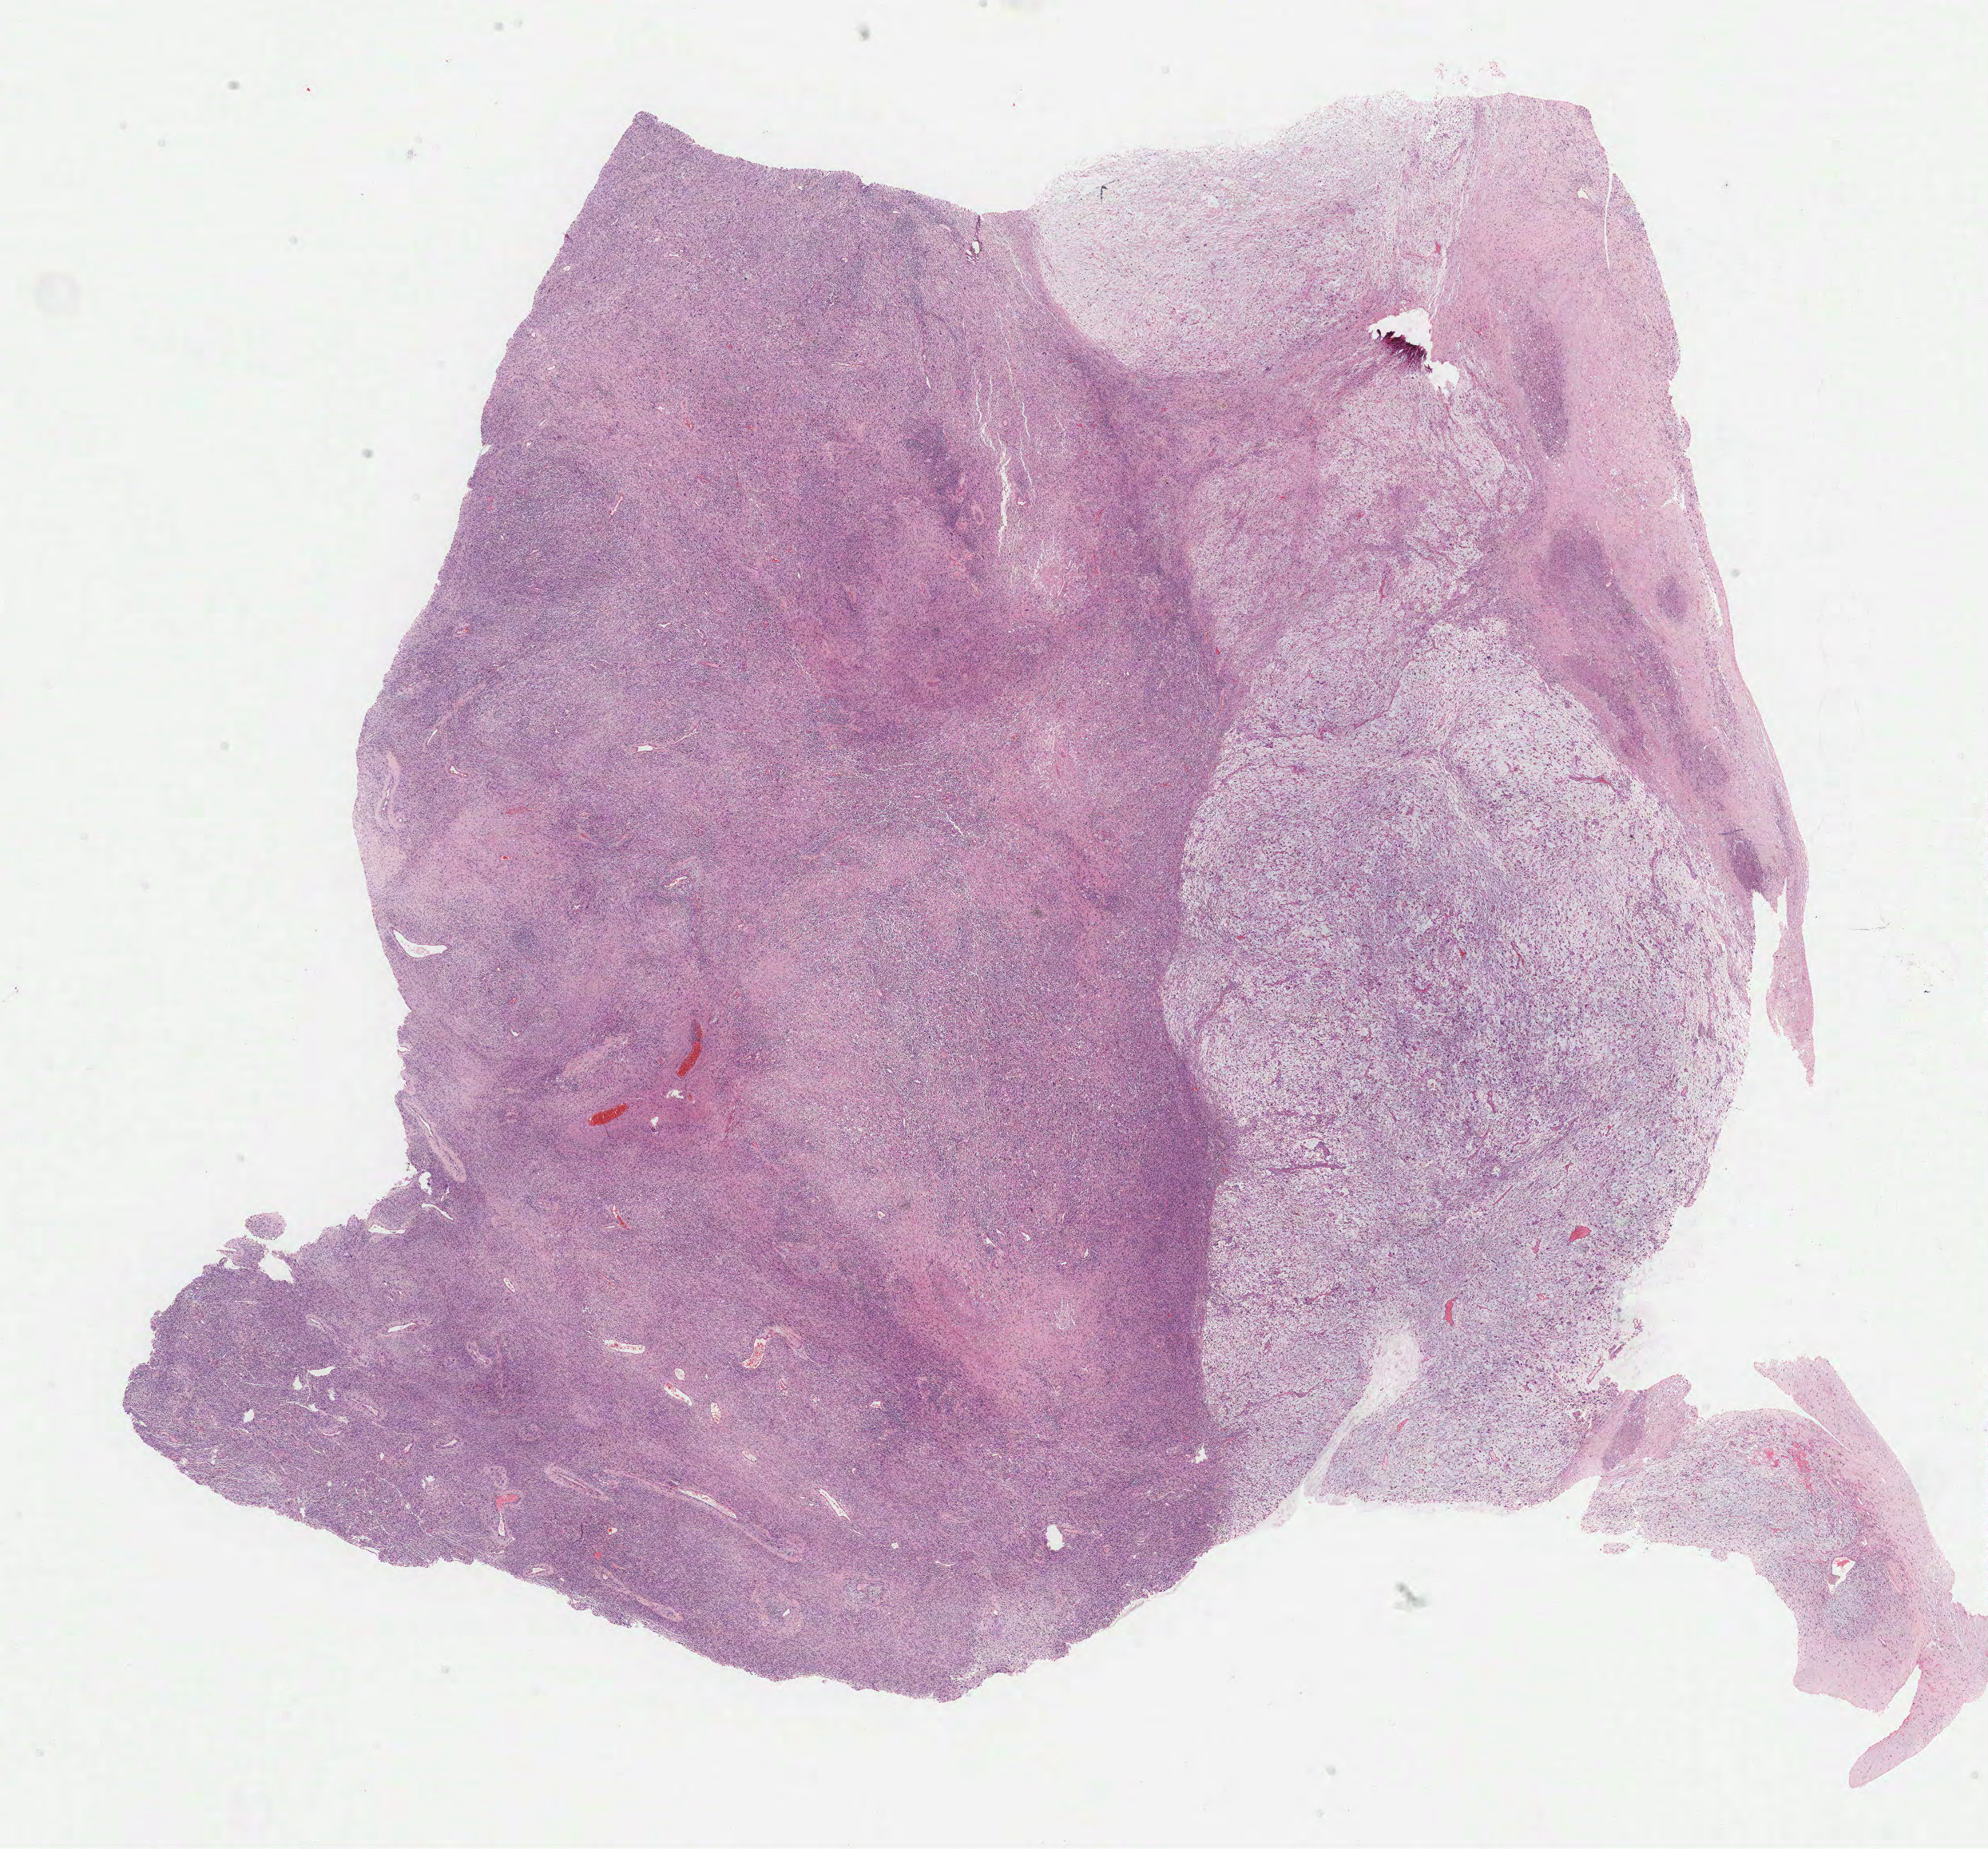
Digitized Hematoxylin and eosin (H&E) stained tissue section (whole slide) — shown as a low-resolution overview of the whole scanned area (about 20.1 x 18.7 mm, acquisition: 40x scan). Formalin-fixed paraffin-embedded (FFPE) diagnostic section. Primary tumour sample from the retroperitoneum and peritoneum. Male patient; age at initial diagnosis 60 years.
• diagnosis: Myxoid leiomyosarcoma (retroperitoneum)